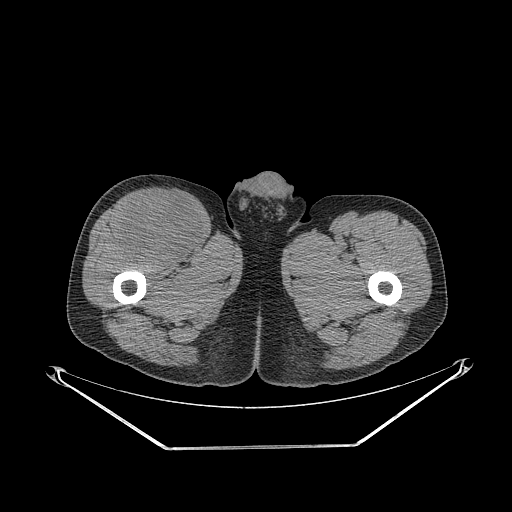
CT of an extremity soft-tissue mass (from a PET/CT study), one axial slice. 140 kVp. Soft-tissue window (W 400 / L 40 HU). 3.75 mm slice thickness. 512 × 512 image matrix, field of view 500 × 500 mm. Male patient. From the clinical record (not read from this slice): histological type: pleiomorphic leiomyosarcoma; grade: intermediate; site of the primary tumour: right thigh.
Structures marked on this image (expert contour drawn on MRI and transferred to this co-registered scan by the dataset authors):
- gross tumour volume including surrounding oedema: bounding box (x1, y1, x2, y2) in pixels: (117, 192, 204, 264)
- gross tumour volume (mass): (119, 192, 204, 264)